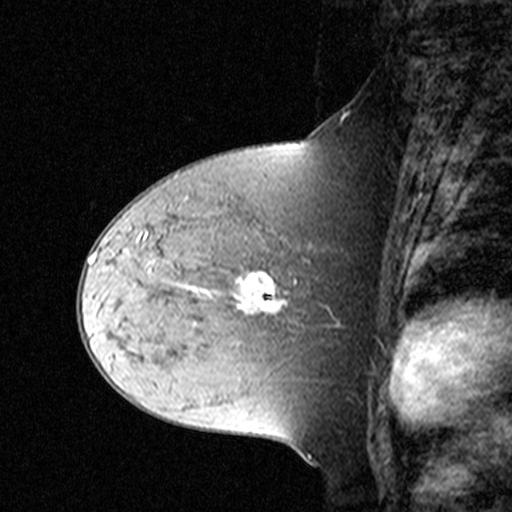
Breast MRI (dynamic contrast-enhanced), one sagittal slice. Position 19 of 44 along the scan axis. Dynamic contrast-enhanced study with each time point stored as its own series, time point 2 of 3 at this slice position (early post-contrast, ordered by acquisition time). 1.5 T. TE 4.5 ms, TR 11 ms. 512 × 512 image matrix, field of view 200 × 200 mm. Patient: female, 44 years. Case-level facts recorded for this patient, not image findings: setting: breast cancer imaged before/during neoadjuvant chemotherapy; receptor status: triple-negative.
Outlined on this slice (semi-automatic segmentation, software-assisted and operator-edited):
- analysis volume of interest (the breast-tissue region the enhancement analysis was run in; not a lesion): bounding box (x1, y1, x2, y2) in pixels: (132, 212, 309, 331)
- tumour enhancement mask (voxels above the 90 % enhancement threshold inside the analysis volume of interest): (241, 272, 287, 313)